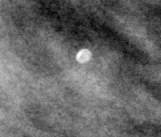
Cropped region of a digitized screen-film mammogram centred on a radiologist-marked abnormality, left breast, MLO view.
Marked abnormality: calcifications, morphology lucent center; BI-RADS assessment category 2; subtlety rating 3 on a 1 (subtle) to 5 (obvious) scale; benign; no additional work-up was recommended (benign without callback).